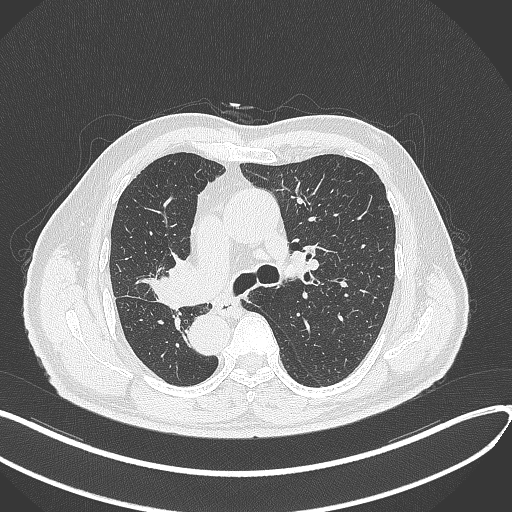
Chest CT, one axial slice. Reconstruction kernel B70f. 120 kVp. Lung window (W 1500 / L -600 HU). 1 mm slice thickness. 512 × 512 image matrix, field of view 400 × 400 mm. Male patient, age 67 years. Case-level facts recorded for this patient, not image findings: clinical TNM (as recorded): T2a N0 M0.
Annotated regions visible in this slice (bounding box drawn by a radiologist):
- lung tumour (recorded histology: squamous cell carcinoma): bounding box [x1, y1, x2, y2] px = [143, 254, 200, 313]